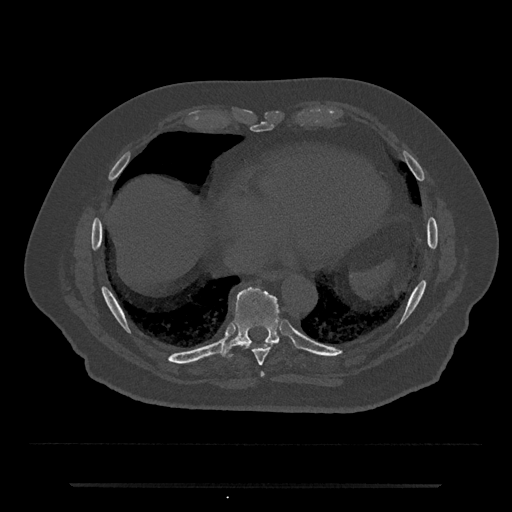
CT including the spine, one axial slice. Slice 778 of 797 in the series (ordered by position). Reconstruction kernel Br40s/3. 120 kVp. Bone window (W 1800 / L 400 HU). 0.5 mm slice thickness. 512 × 512 image matrix, field of view 434 × 434 mm. Patient: male, 80 years. From the clinical record (not read from this slice): primary cancer: prostate; vertebrae with lytic lesions (as recorded): L1, T11.
Annotated regions visible in this slice (semi-automatically segmented with operator editing):
- T8 vertebra: bounding box <247,343,277,366> (left, top, right, bottom; pixels)
- T9 vertebra: <218,287,281,359>